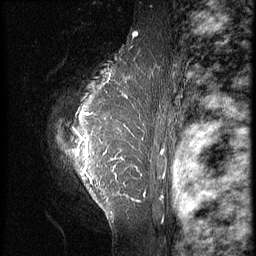
Breast MRI (dynamic contrast-enhanced), one sagittal slice; position 50 of 64 along the scan axis; 3 images stored at this slice position (order not interpretable as contrast timing); 1.5 T; TE 4.2 ms, TR 9 ms; 256 × 256 image matrix, field of view 180 × 180 mm. Female patient, age 39 years. From the clinical record (not read from this slice): setting: breast cancer imaged before/during neoadjuvant chemotherapy; receptor status: HER2-positive.
Outlined on this slice (semi-automatically segmented with operator editing):
- analysis volume of interest (the breast-tissue region the enhancement analysis was run in; not a lesion): bounding box [x1, y1, x2, y2] px = [46, 47, 149, 239]
- tumour enhancement mask (voxels above the 140 % enhancement threshold inside the analysis volume of interest): [79, 112, 136, 172]